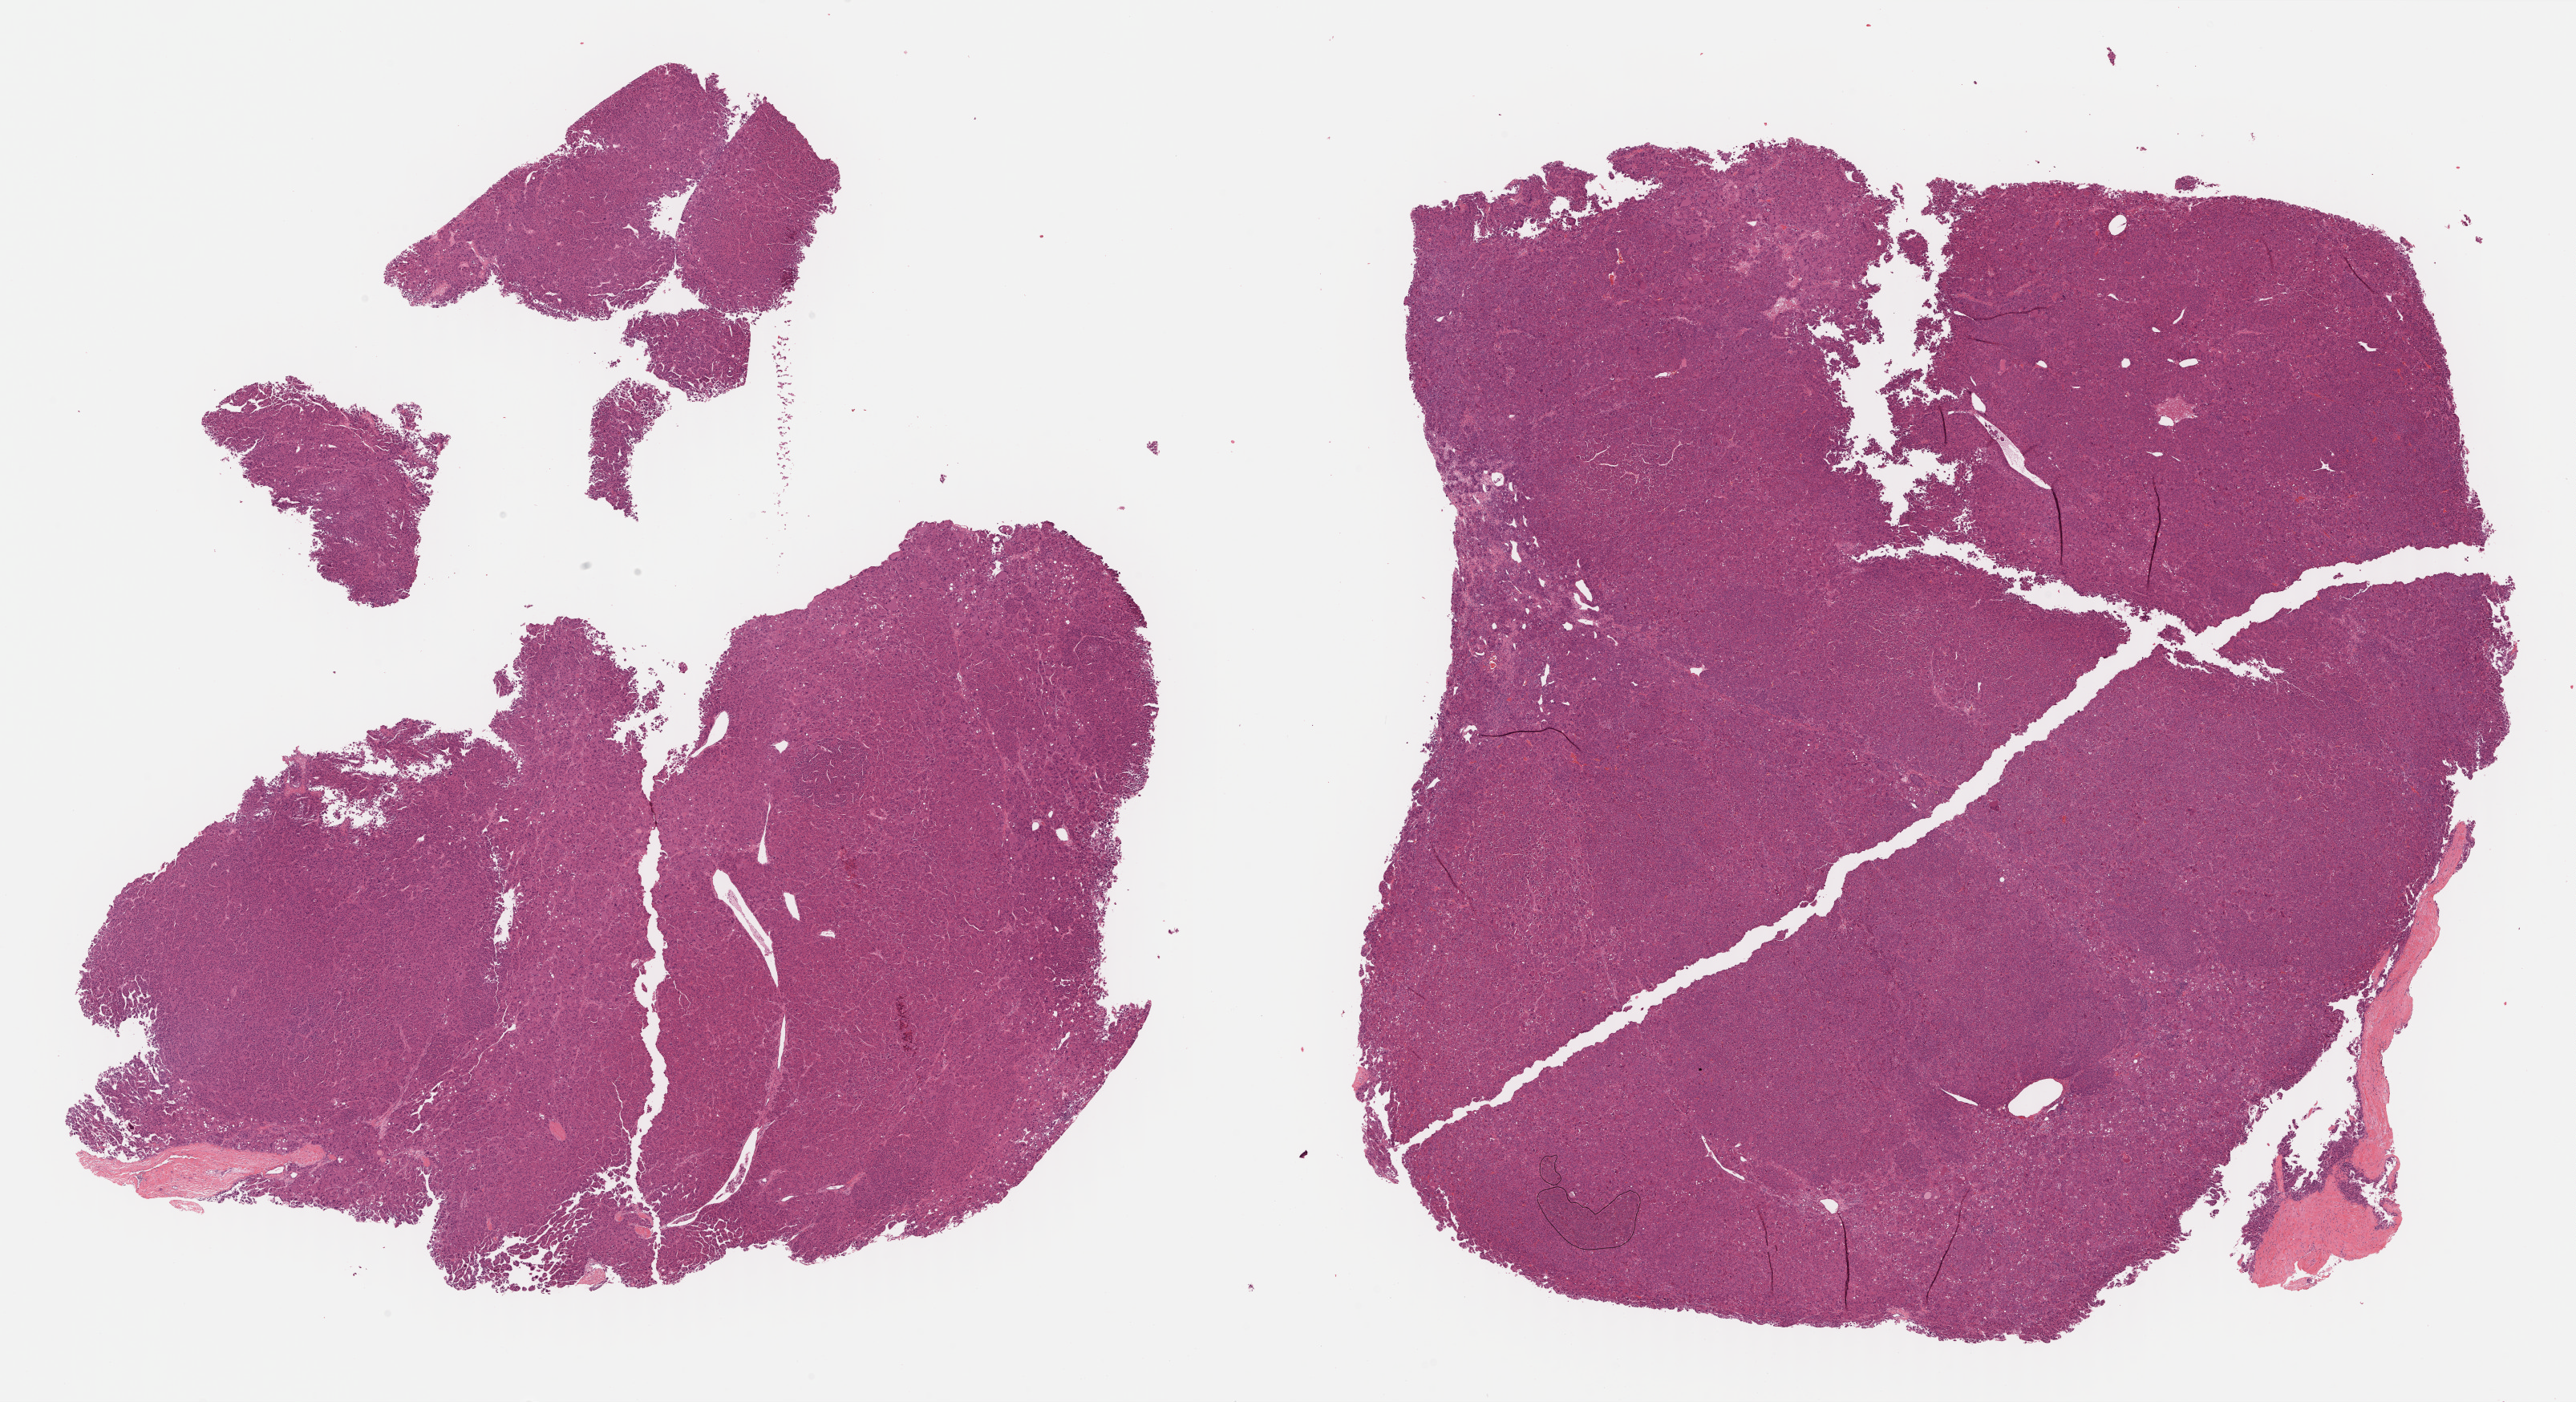
Whole-slide histology image, Hematoxylin and eosin (H&E) stained — low-resolution overview of the scanned area, about 26.0 x 14.2 mm; FFPE section; primary tumour sample from the liver. Male, age 73 years at initial diagnosis. Histologic grade: G3 (poorly differentiated).
* AJCC pathologic stage: IIIA (6th edition)
* TNM: T3 N0 M0
* histologic diagnosis: Hepatocellular carcinoma, NOS